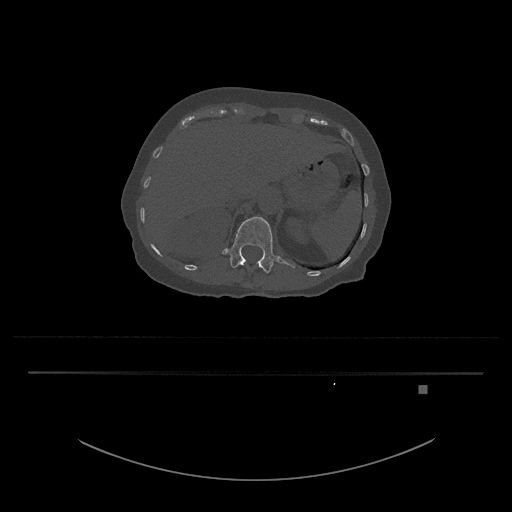
CT including the spine, one axial slice. Position 565 of 797 along the scan axis. Reconstruction kernel Br40s/3. 120 kVp. Bone window (W 1800 / L 400 HU). 512 × 512 image matrix, field of view 500 × 500 mm. Patient: female, 57 years. From the clinical record (not read from this slice): primary cancer: cervical.
Annotated regions visible in this slice (semi-automatically segmented with operator editing):
- L1 vertebra: box from (x=222, y=217) to (x=295, y=273) px
- T12 vertebra: (x=243, y=263)–(x=261, y=268)